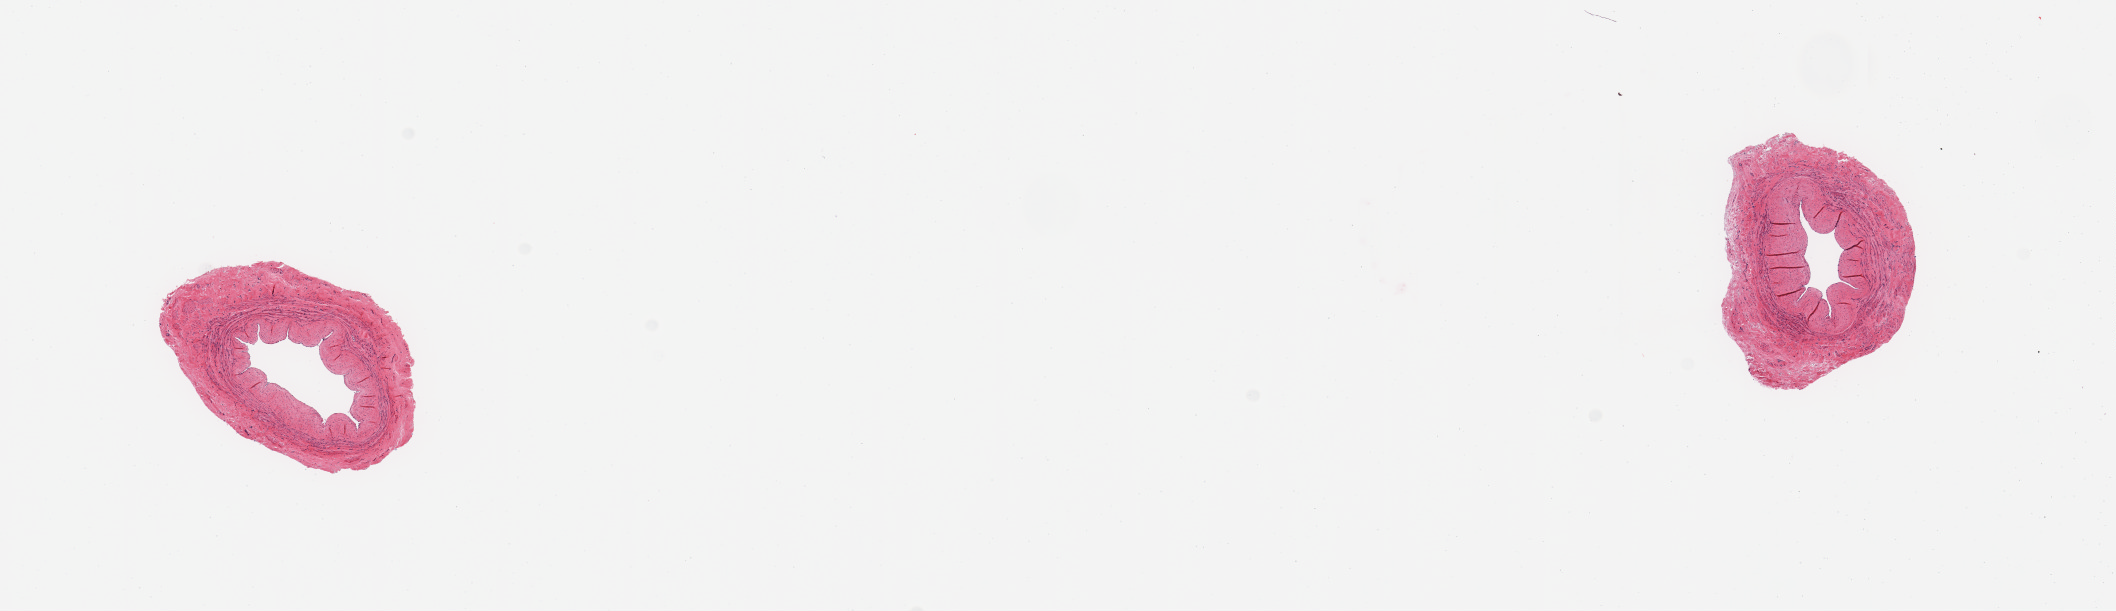
Digitized H&E-stained section, brightfield — whole scanned area (about 16.7 x 4.8 mm) shown as a low-resolution overview. PAXgene-fixed, paraffin-embedded tissue. Section of tibial artery (target tissue). Donor tissue sample. Male donor.
Pathologist's review note for this sample: 2 pieces; no plaques; preserved endothelium; well trimmed.